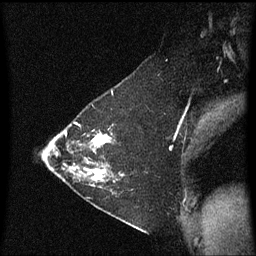
Breast MRI (dynamic contrast-enhanced), one sagittal slice; slice 42 of 60 in the series (ordered by position); dynamic contrast-enhanced series, image 2 of 3 at this slice position (ordered by acquisition); 1.5 T; TE 4.2 ms, TR 8.4 ms; 2 mm slice thickness; 256 × 256 image matrix, field of view 200 × 200 mm. Patient: female, 36 years. From the clinical record (not read from this slice): setting: breast cancer imaged before/during neoadjuvant chemotherapy; receptor status: HR-positive, HER2-negative.
Outlined on this slice (semi-automatically segmented with operator editing):
- analysis volume of interest (the breast-tissue region the enhancement analysis was run in; not a lesion): bounding box (x1, y1, x2, y2) in pixels: (72, 116, 123, 187)
- tumour enhancement mask (voxels above the 70 % enhancement threshold inside the analysis volume of interest): (86, 132, 123, 183)